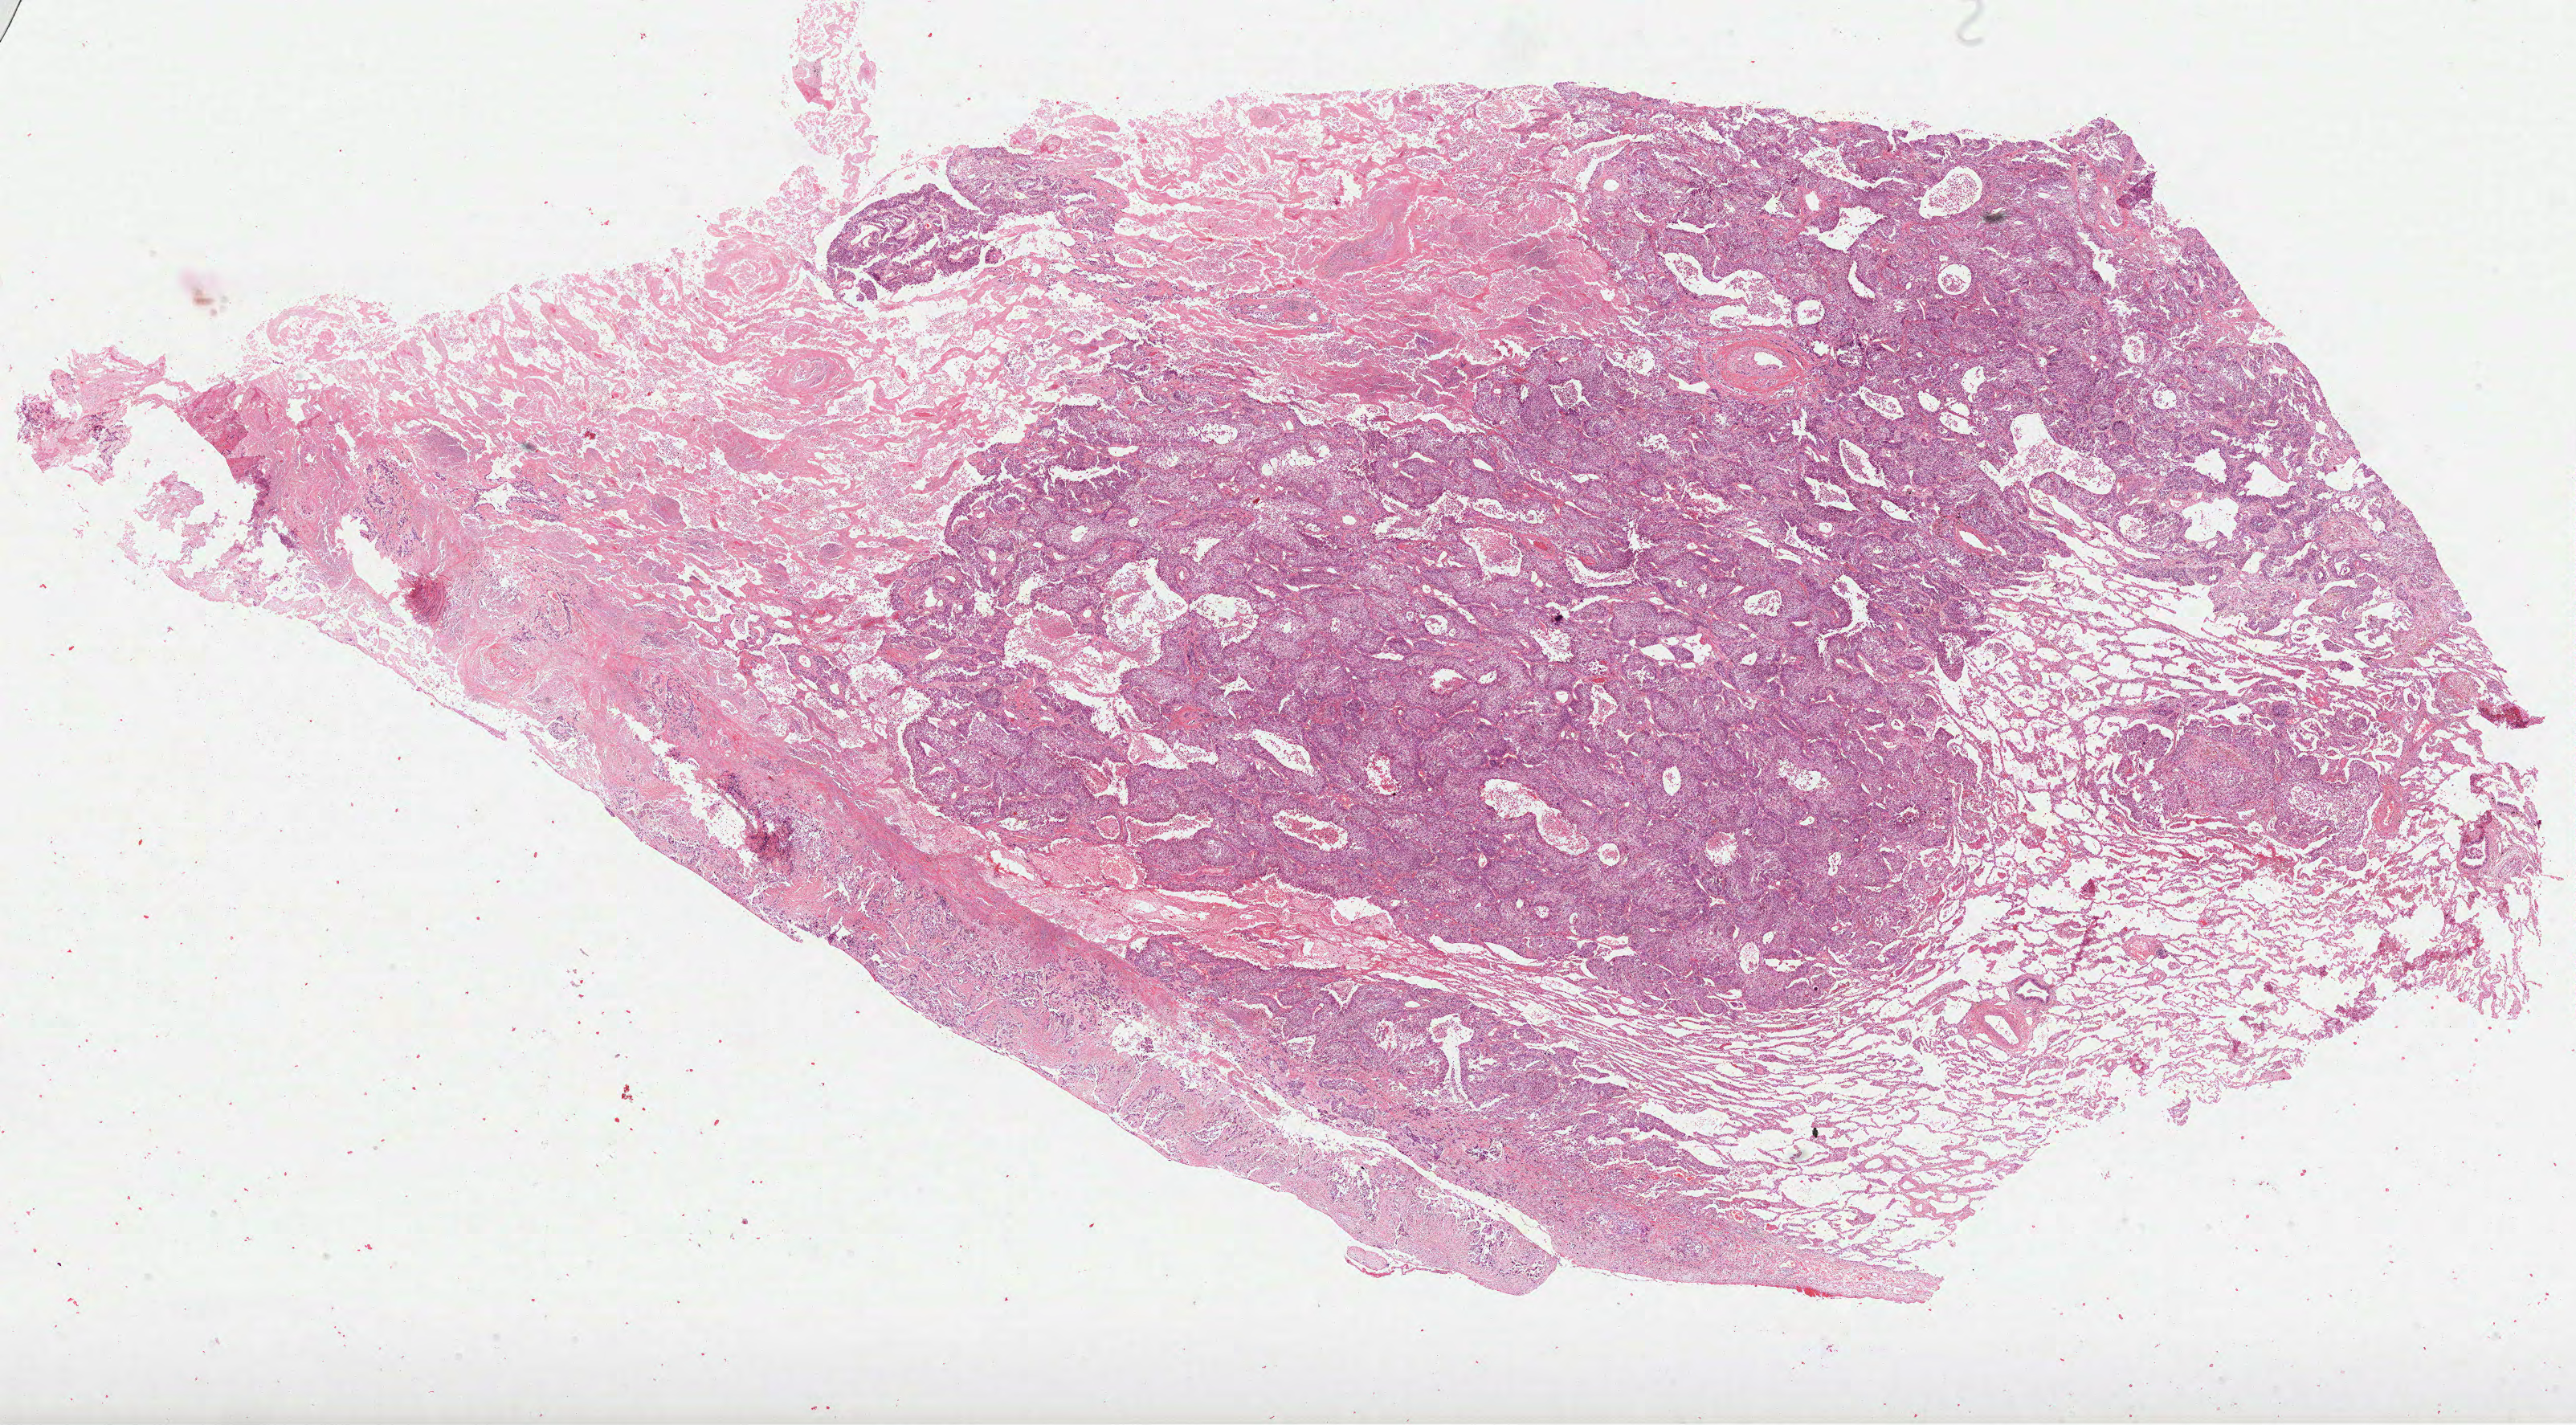
H&E whole-slide image, low-resolution overview of the scanned area, about 25.9 x 14.3 mm (slide scanned at 40x), formalin-fixed paraffin-embedded (FFPE) diagnostic section, primary tumour sample from the lung. Male, age 72 years at initial diagnosis.
Pathologic diagnosis: Squamous cell carcinoma, NOS (lower lobe, lung).